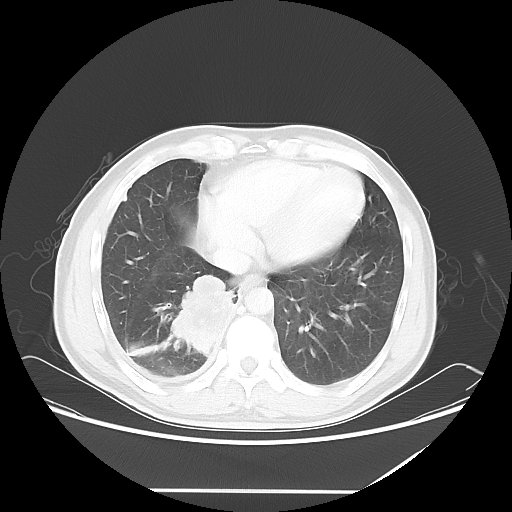
Chest CT, one axial slice; position 20 of 60 along the scan axis; reconstruction kernel LUNG; 120 kVp; lung window (W 1500 / L -600 HU); 5 mm slice thickness; 512 × 512 image matrix. Patient: male, 48 years. Case-level facts recorded for this patient, not image findings: clinical TNM (as recorded): T3 N3 M1a.
Outlined on this slice (rectangle marked by the reading radiologist):
- lung tumour (recorded histology: squamous cell carcinoma): bounding box [x1, y1, x2, y2] px = [162, 273, 236, 364]